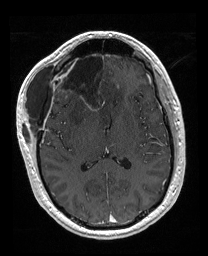
Brain MRI from a brain-tumour surgery series, one axial slice. Position 89 of 176 along the scan axis. T1-weighted post-contrast. 1 mm slice thickness. 208 × 256 image matrix, field of view 208 × 256 mm. From the clinical record (not read from this slice): histopathology: Astrocytoma; WHO grade: 4; IDH mutation: yes; tumour location: Right Orbitofrontal Anterior Temporal Insular.
Annotated regions visible in this slice (expert manual segmentation):
- previous resection cavity: box from (x=56, y=52) to (x=106, y=111) px